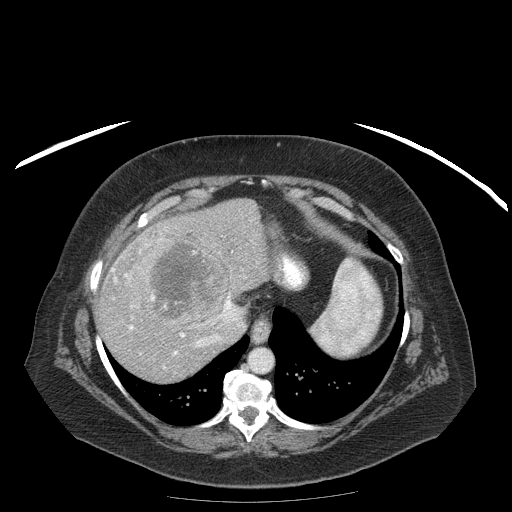
Contrast-enhanced abdominal CT (liver protocol), one axial slice; slice 149 of 204 in the series (ordered by position); soft-tissue window (W 400 / L 40 HU); 2.5 mm slice thickness; 512 × 512 image matrix, field of view 440 × 440 mm. From the clinical record (not read from this slice): diagnosis: hepatocellular carcinoma (patient treated with transarterial chemoembolisation; whether this scan precedes or follows treatment is not stated here); TNM stage (as recorded): Stage-IIIB; Child-Pugh class: A; tumour differentiation: well differentiated.
Outlined on this slice (semi-automatic segmentation, software-assisted and operator-edited):
- liver parenchyma outside the tumour (the mass and vessels are separate outlines, so this box may not span the whole liver): box from (x=96, y=198) to (x=278, y=382) px
- mass: (x=129, y=234)–(x=230, y=331)
- liver vessels: (x=111, y=250)–(x=241, y=368)